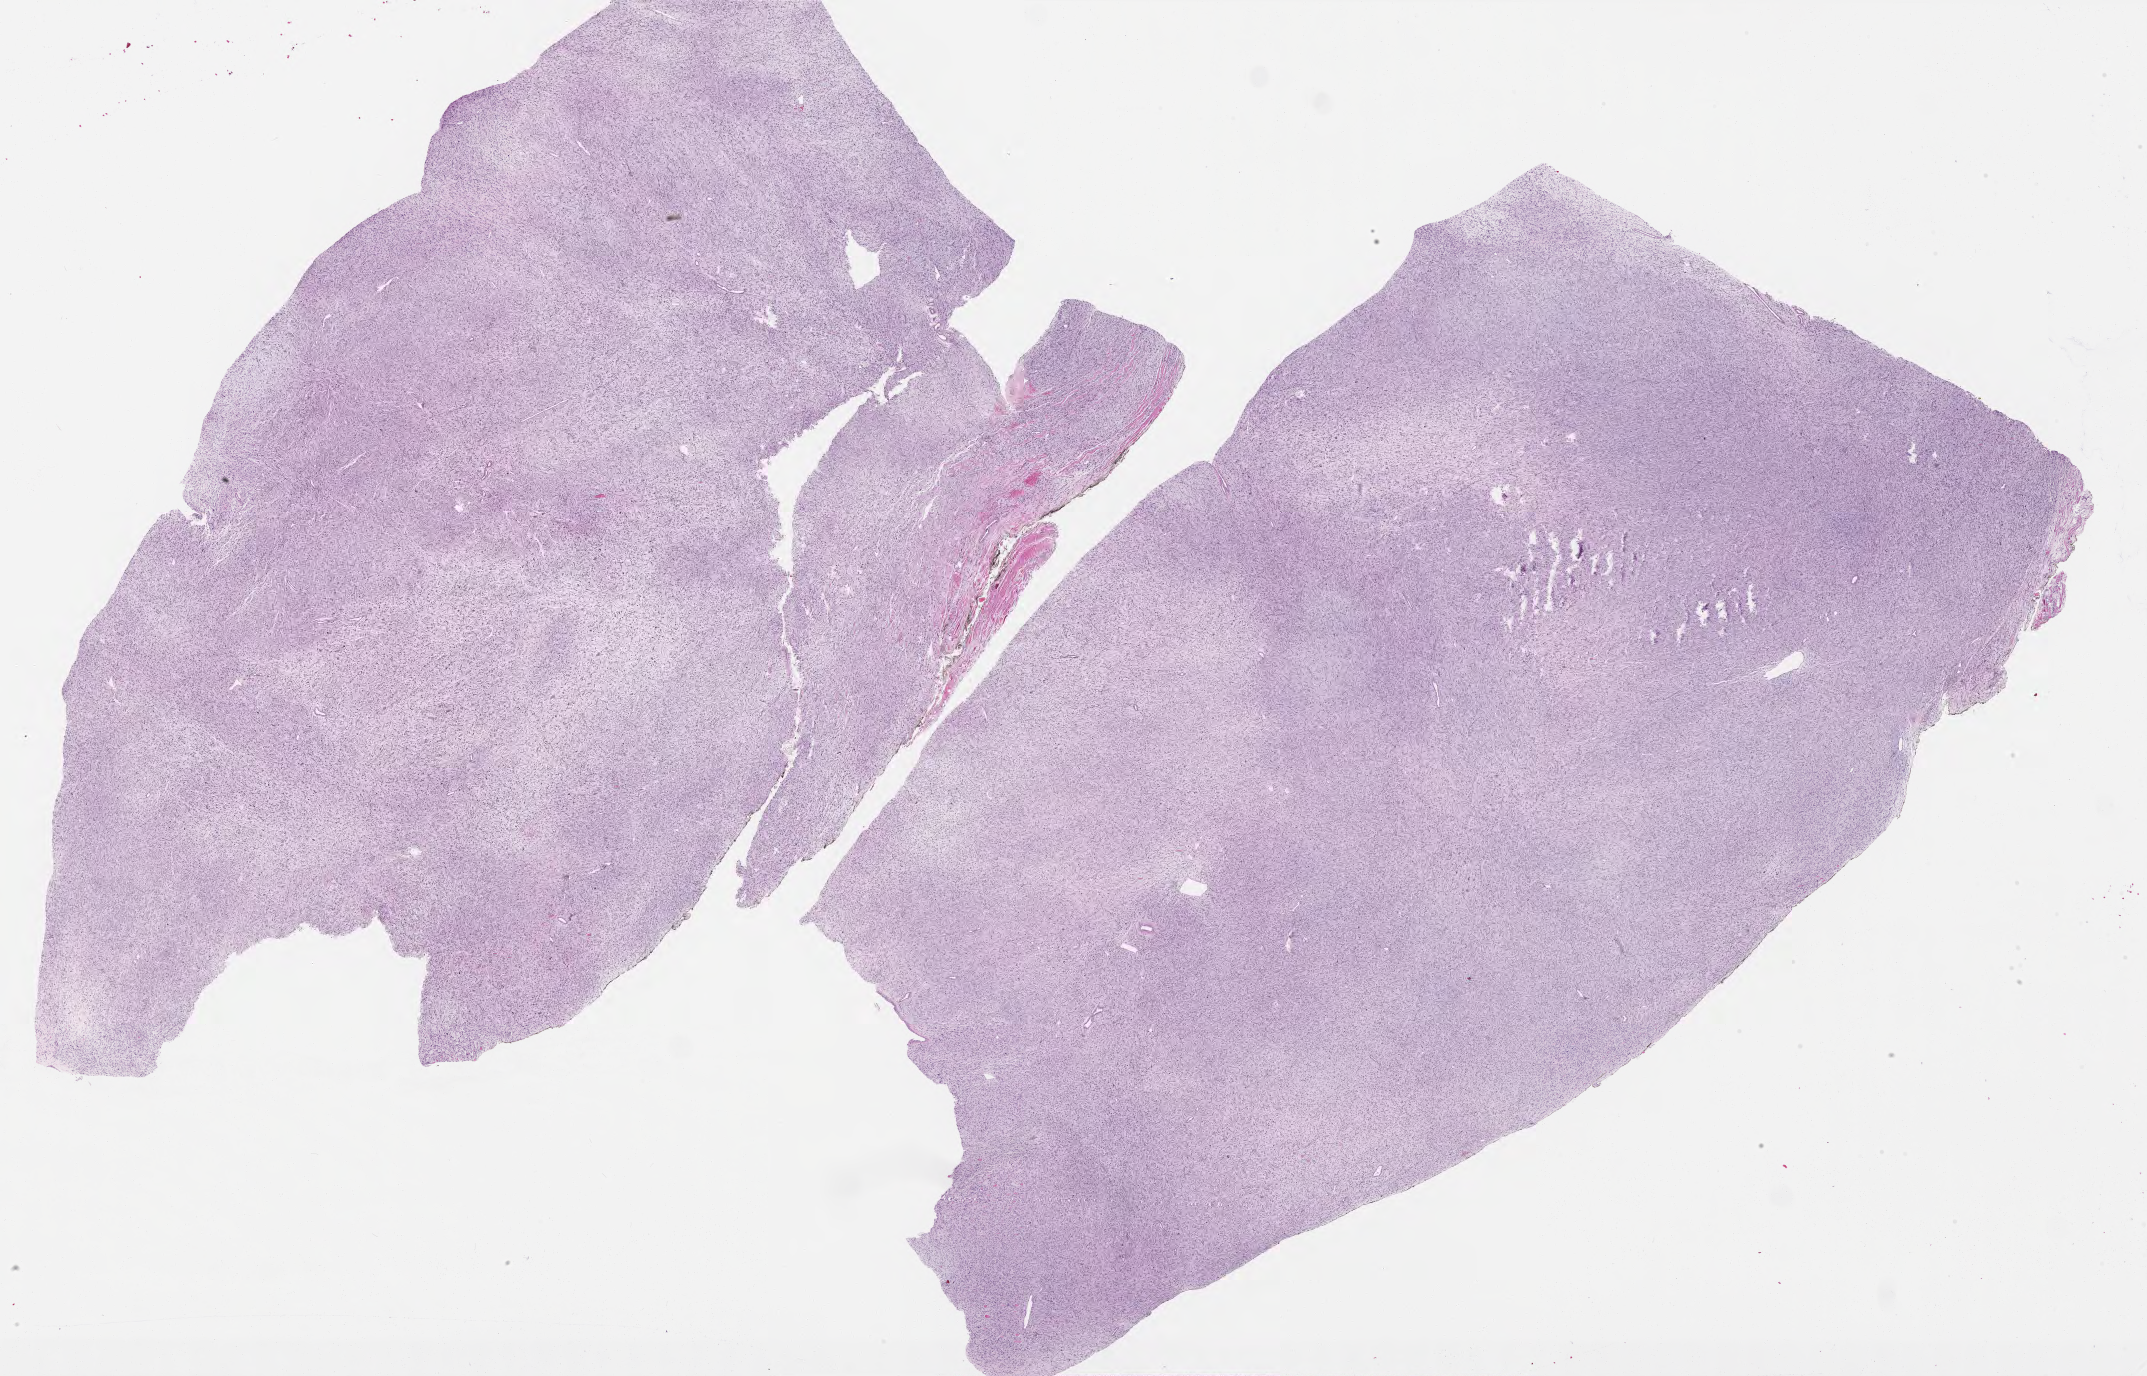
Digitized Hematoxylin and eosin (H&E) stained tissue section (whole slide) — whole scanned area (about 34.5 x 22.1 mm) shown as a low-resolution overview; formalin-fixed paraffin-embedded (FFPE) diagnostic section; primary tumour sample from the retroperitoneum and peritoneum. Patient: female, age at initial diagnosis 79 years.
- diagnosis: Fibromyxosarcoma (retroperitoneum)